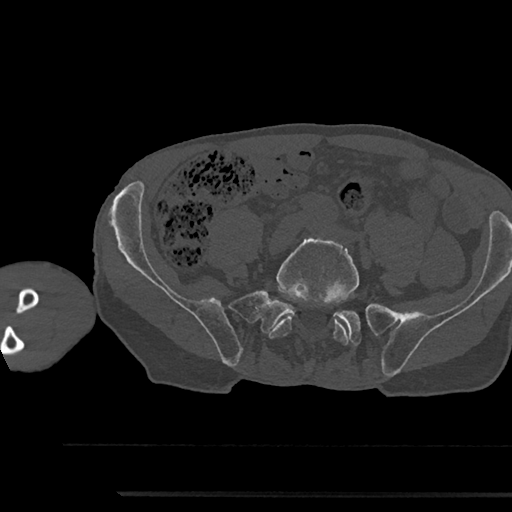
CT including the spine, one axial slice. Slice 325 of 797 in the series (ordered by position). Bone window (W 1800 / L 400 HU). 0.5 mm slice thickness. 512 × 512 image matrix, field of view 367 × 367 mm. Male patient, age 79 years. Case-level facts recorded for this patient, not image findings: primary cancer: prostate.
Annotated regions visible in this slice (semi-automatic segmentation, software-assisted and operator-edited):
- L5 vertebra: bounding box <268,236,359,345> (left, top, right, bottom; pixels)